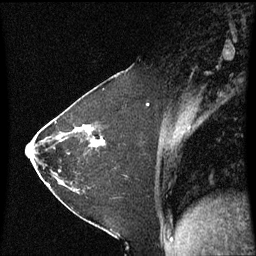
Breast MRI (dynamic contrast-enhanced), one sagittal slice. Dynamic contrast-enhanced series, image 2 of 3 at this slice position (ordered by acquisition). 1.5 T. TE 4.2 ms, TR 8.9 ms. 2 mm slice thickness. 256 × 256 image matrix, field of view 200 × 200 mm. Female patient, age 37 years. Case-level facts recorded for this patient, not image findings: setting: breast cancer imaged before/during neoadjuvant chemotherapy; receptor status: HR-positive, HER2-negative.
Structures marked on this image (semi-automatic segmentation, software-assisted and operator-edited):
- analysis volume of interest (the breast-tissue region the enhancement analysis was run in; not a lesion): box from (x=60, y=102) to (x=122, y=181) px
- tumour enhancement mask (voxels above the 70 % enhancement threshold inside the analysis volume of interest): (x=92, y=132)–(x=100, y=147)